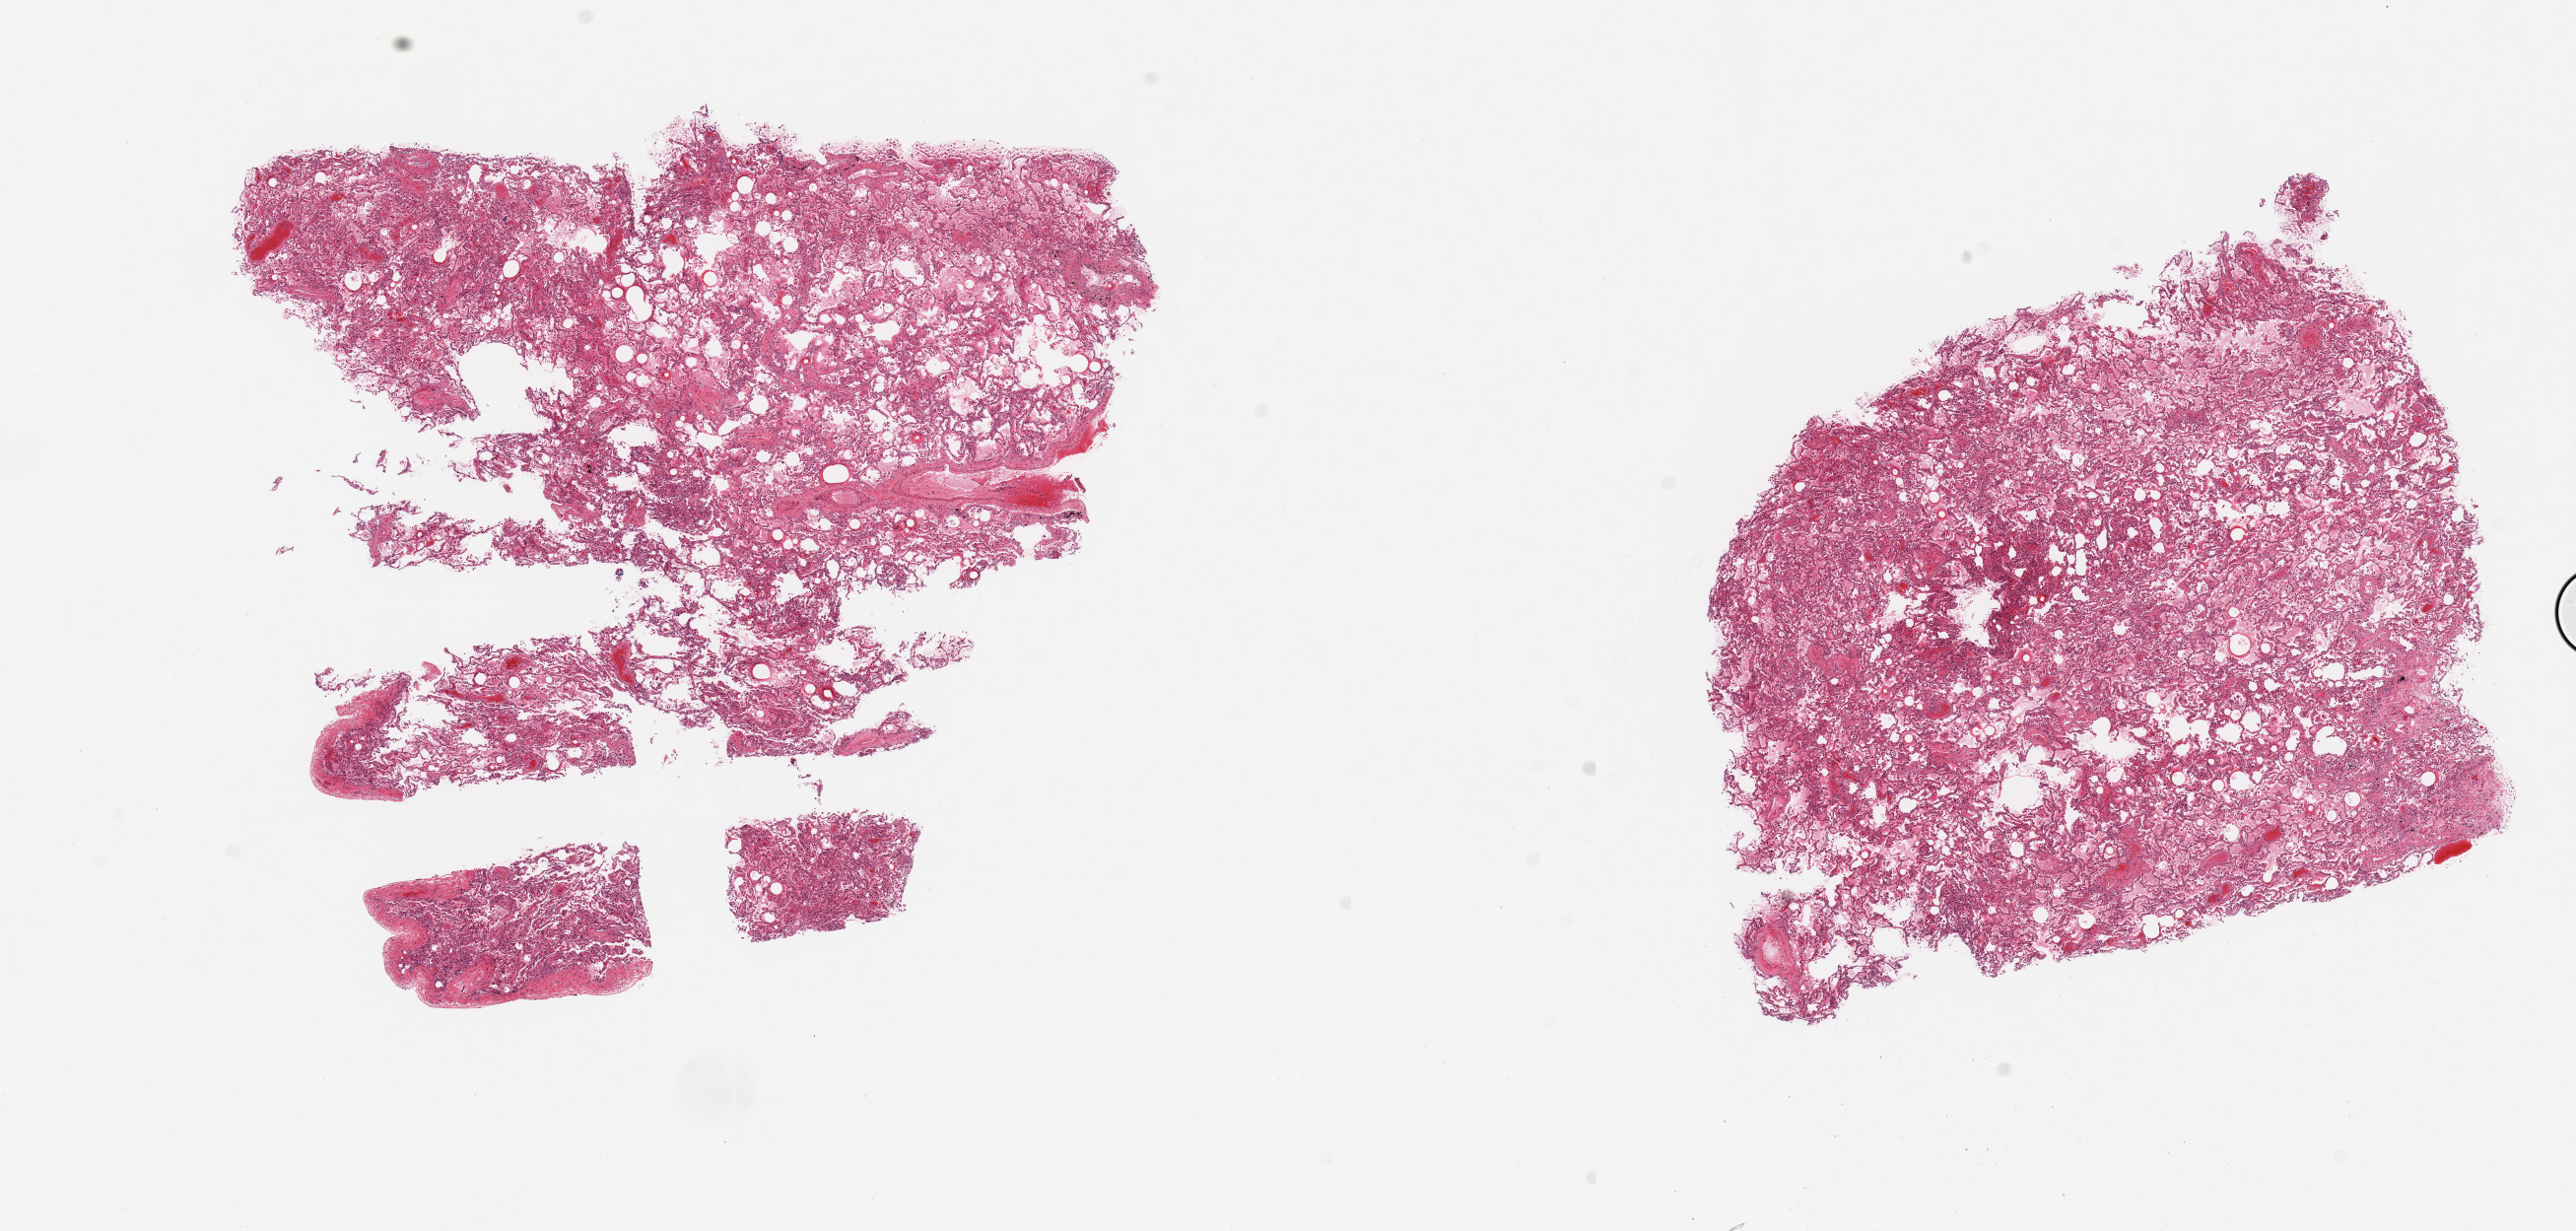
Digitized haematoxylin and eosin-stained section, brightfield — a low-resolution overview of the entire scanned area, about 20.7 x 9.9 mm; PAXgene-fixed paraffin-embedded (PFPE) section; section of lung (target tissue); tissue donor sample. Male donor.
Reviewer comment on this tissue sample: 2 pieces; congestion and edema; numerous macrophages, attached pleura.